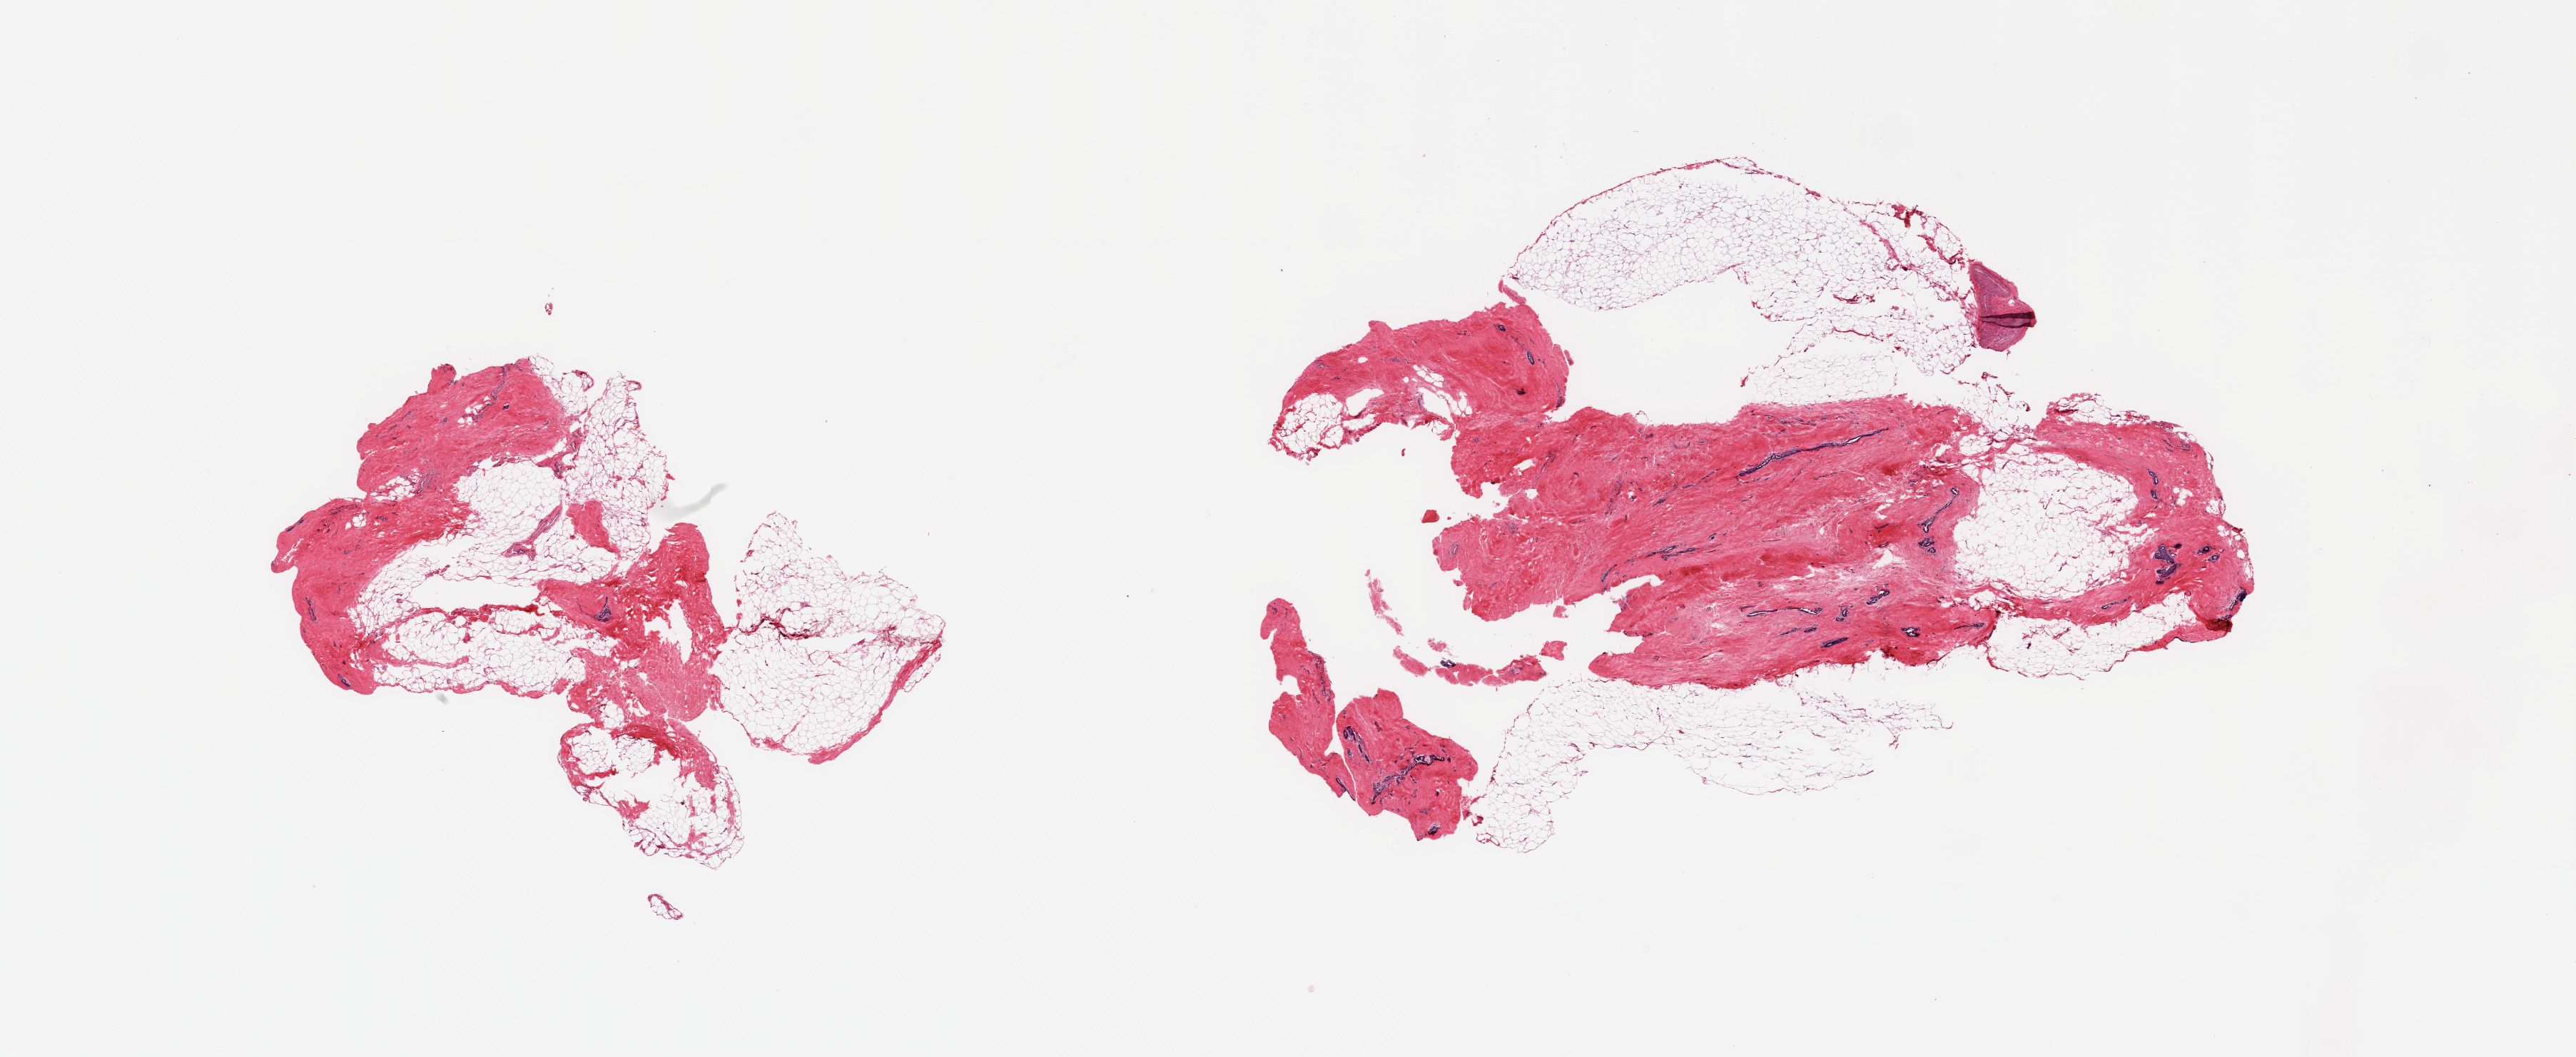
Digitized hematoxylin and eosin (H&E)-stained section — shown as a low-resolution overview of the whole scanned area (about 28.5 x 11.7 mm); PAXgene-fixed, paraffin-embedded tissue; sampled site (target tissue): breast; donor tissue sample. Male donor.
* reviewer comment on this tissue sample: 2 pieces gynecomastoid stromal and ductal hyperplasia